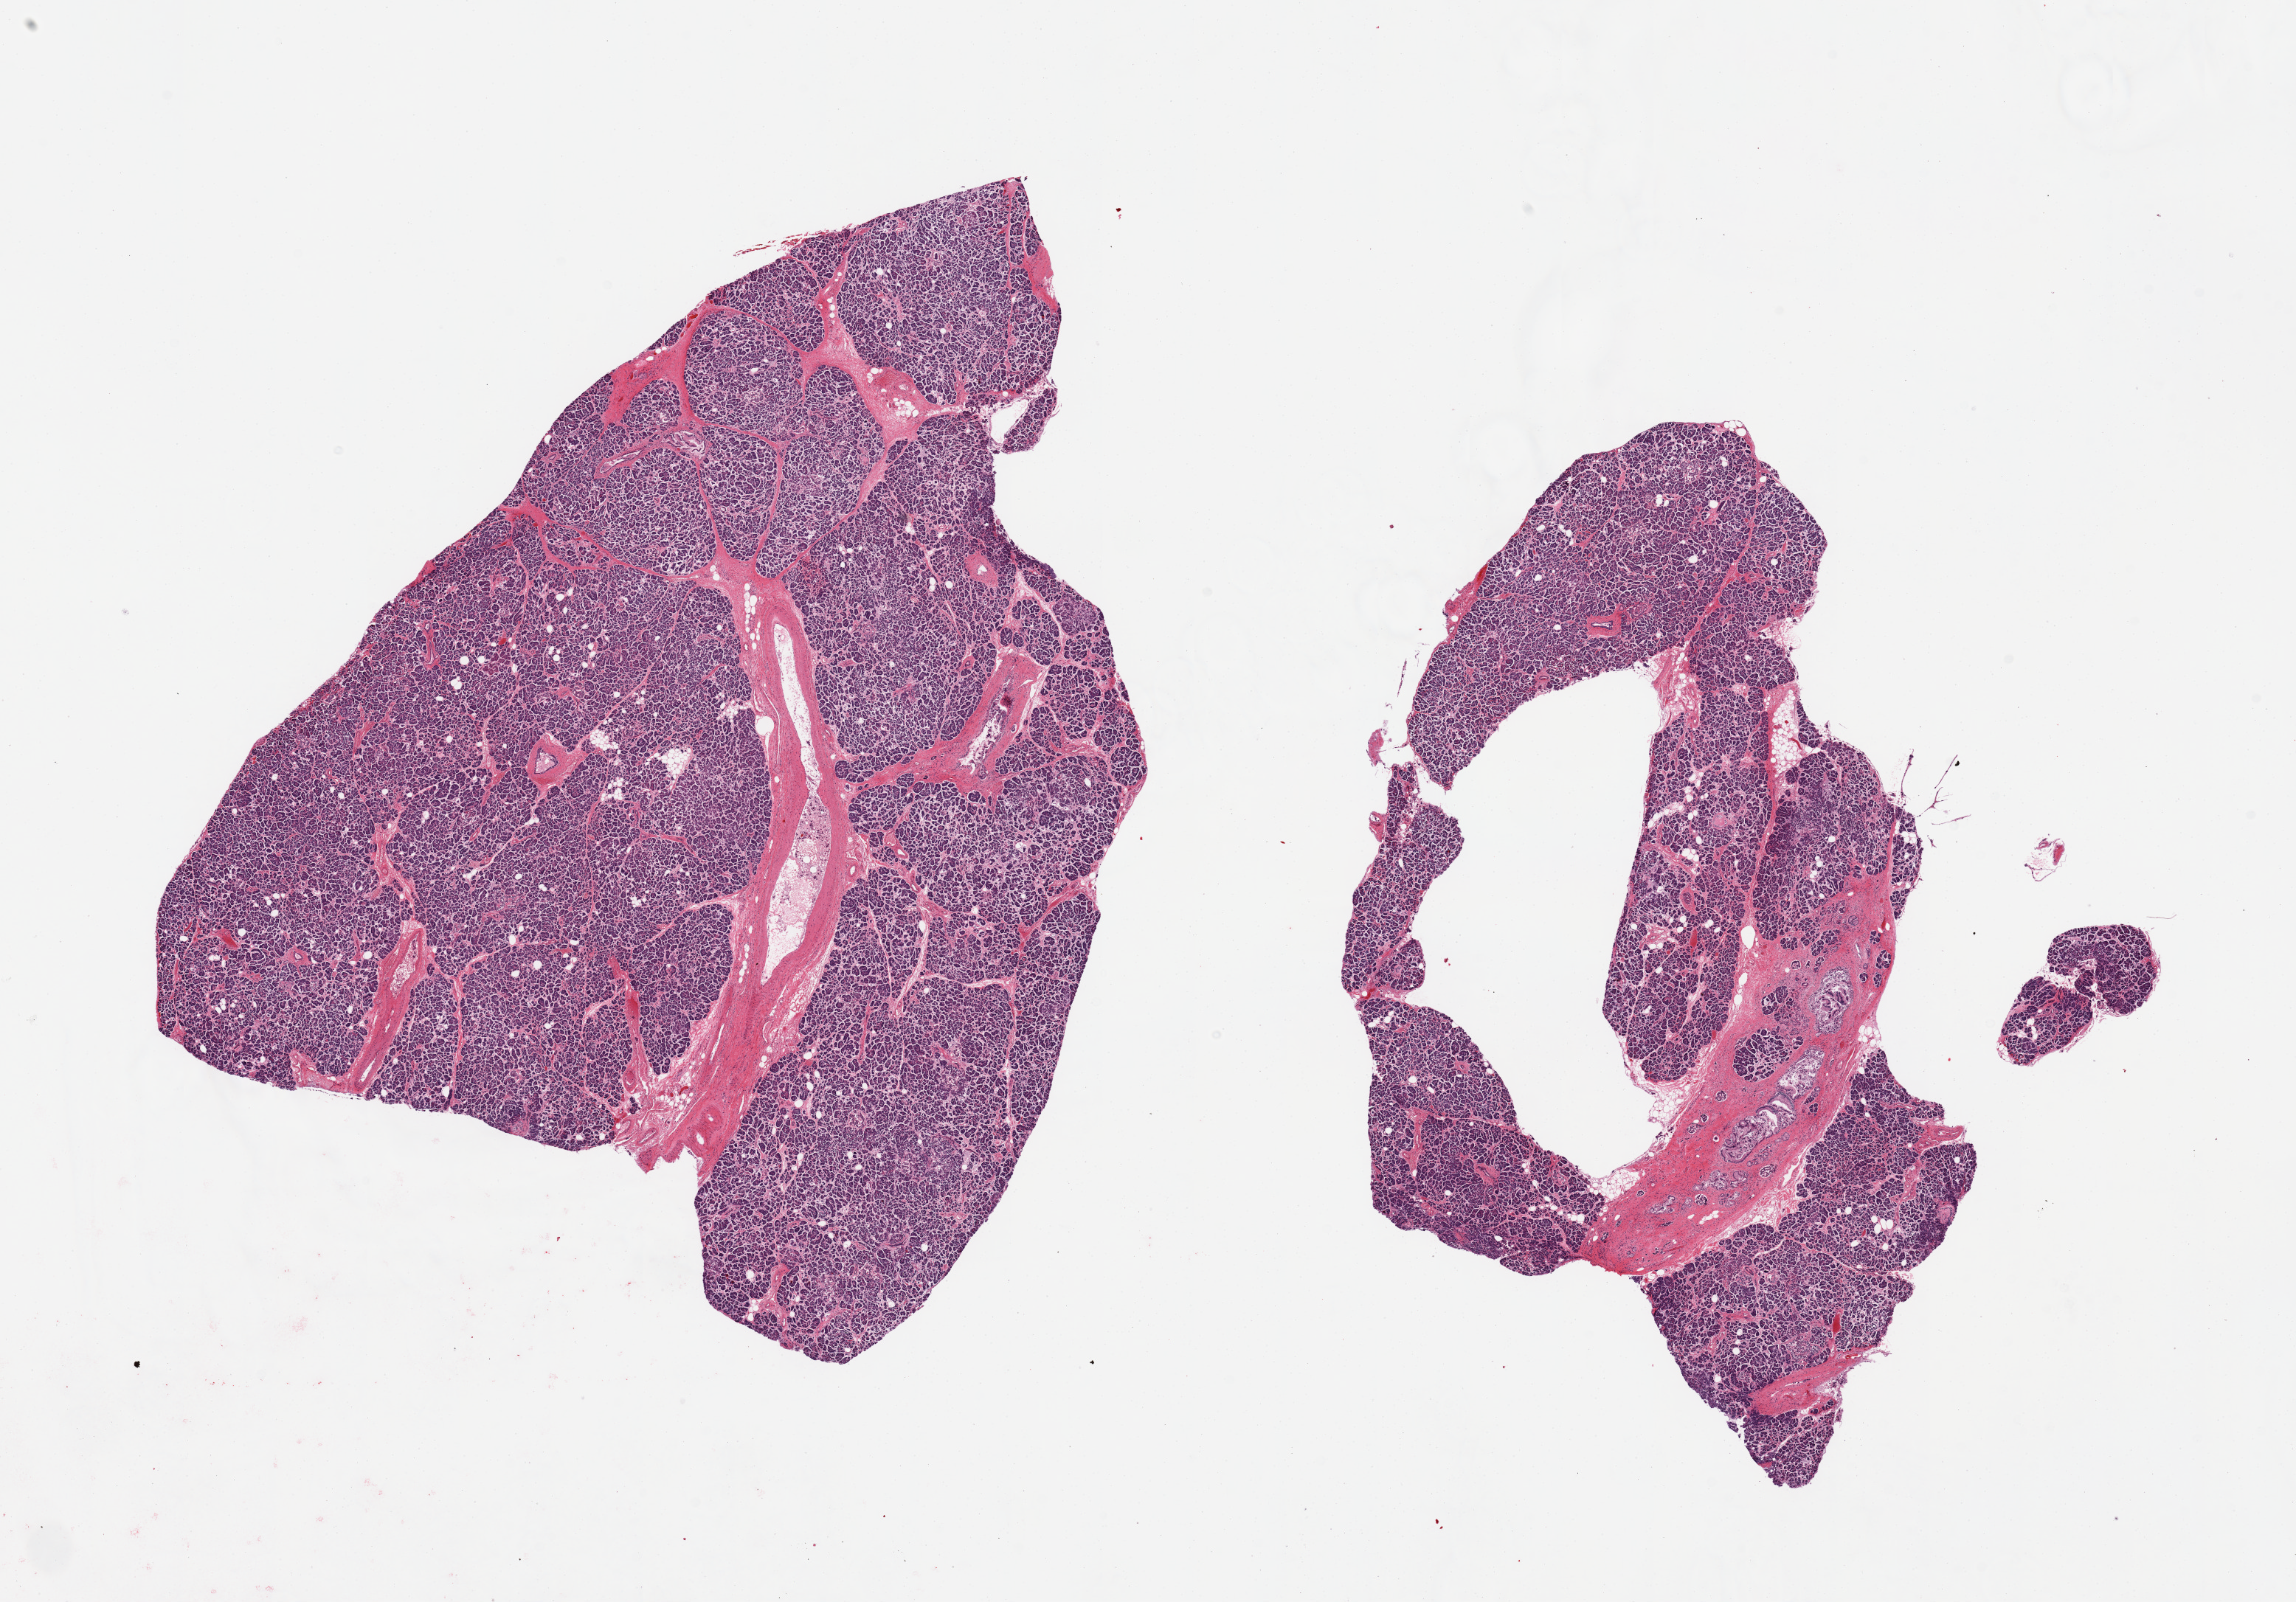
Whole-slide image, haematoxylin and eosin stain, whole scanned area (about 24.6 x 17.2 mm) shown as a low-resolution overview, PAXgene-fixed paraffin-embedded (PFPE) section, target tissue: pancreas, donor tissue sample. Donor sex: female.
Reviewer comment on this tissue sample: 2 pieces; ducts have PanIN 1 changes.